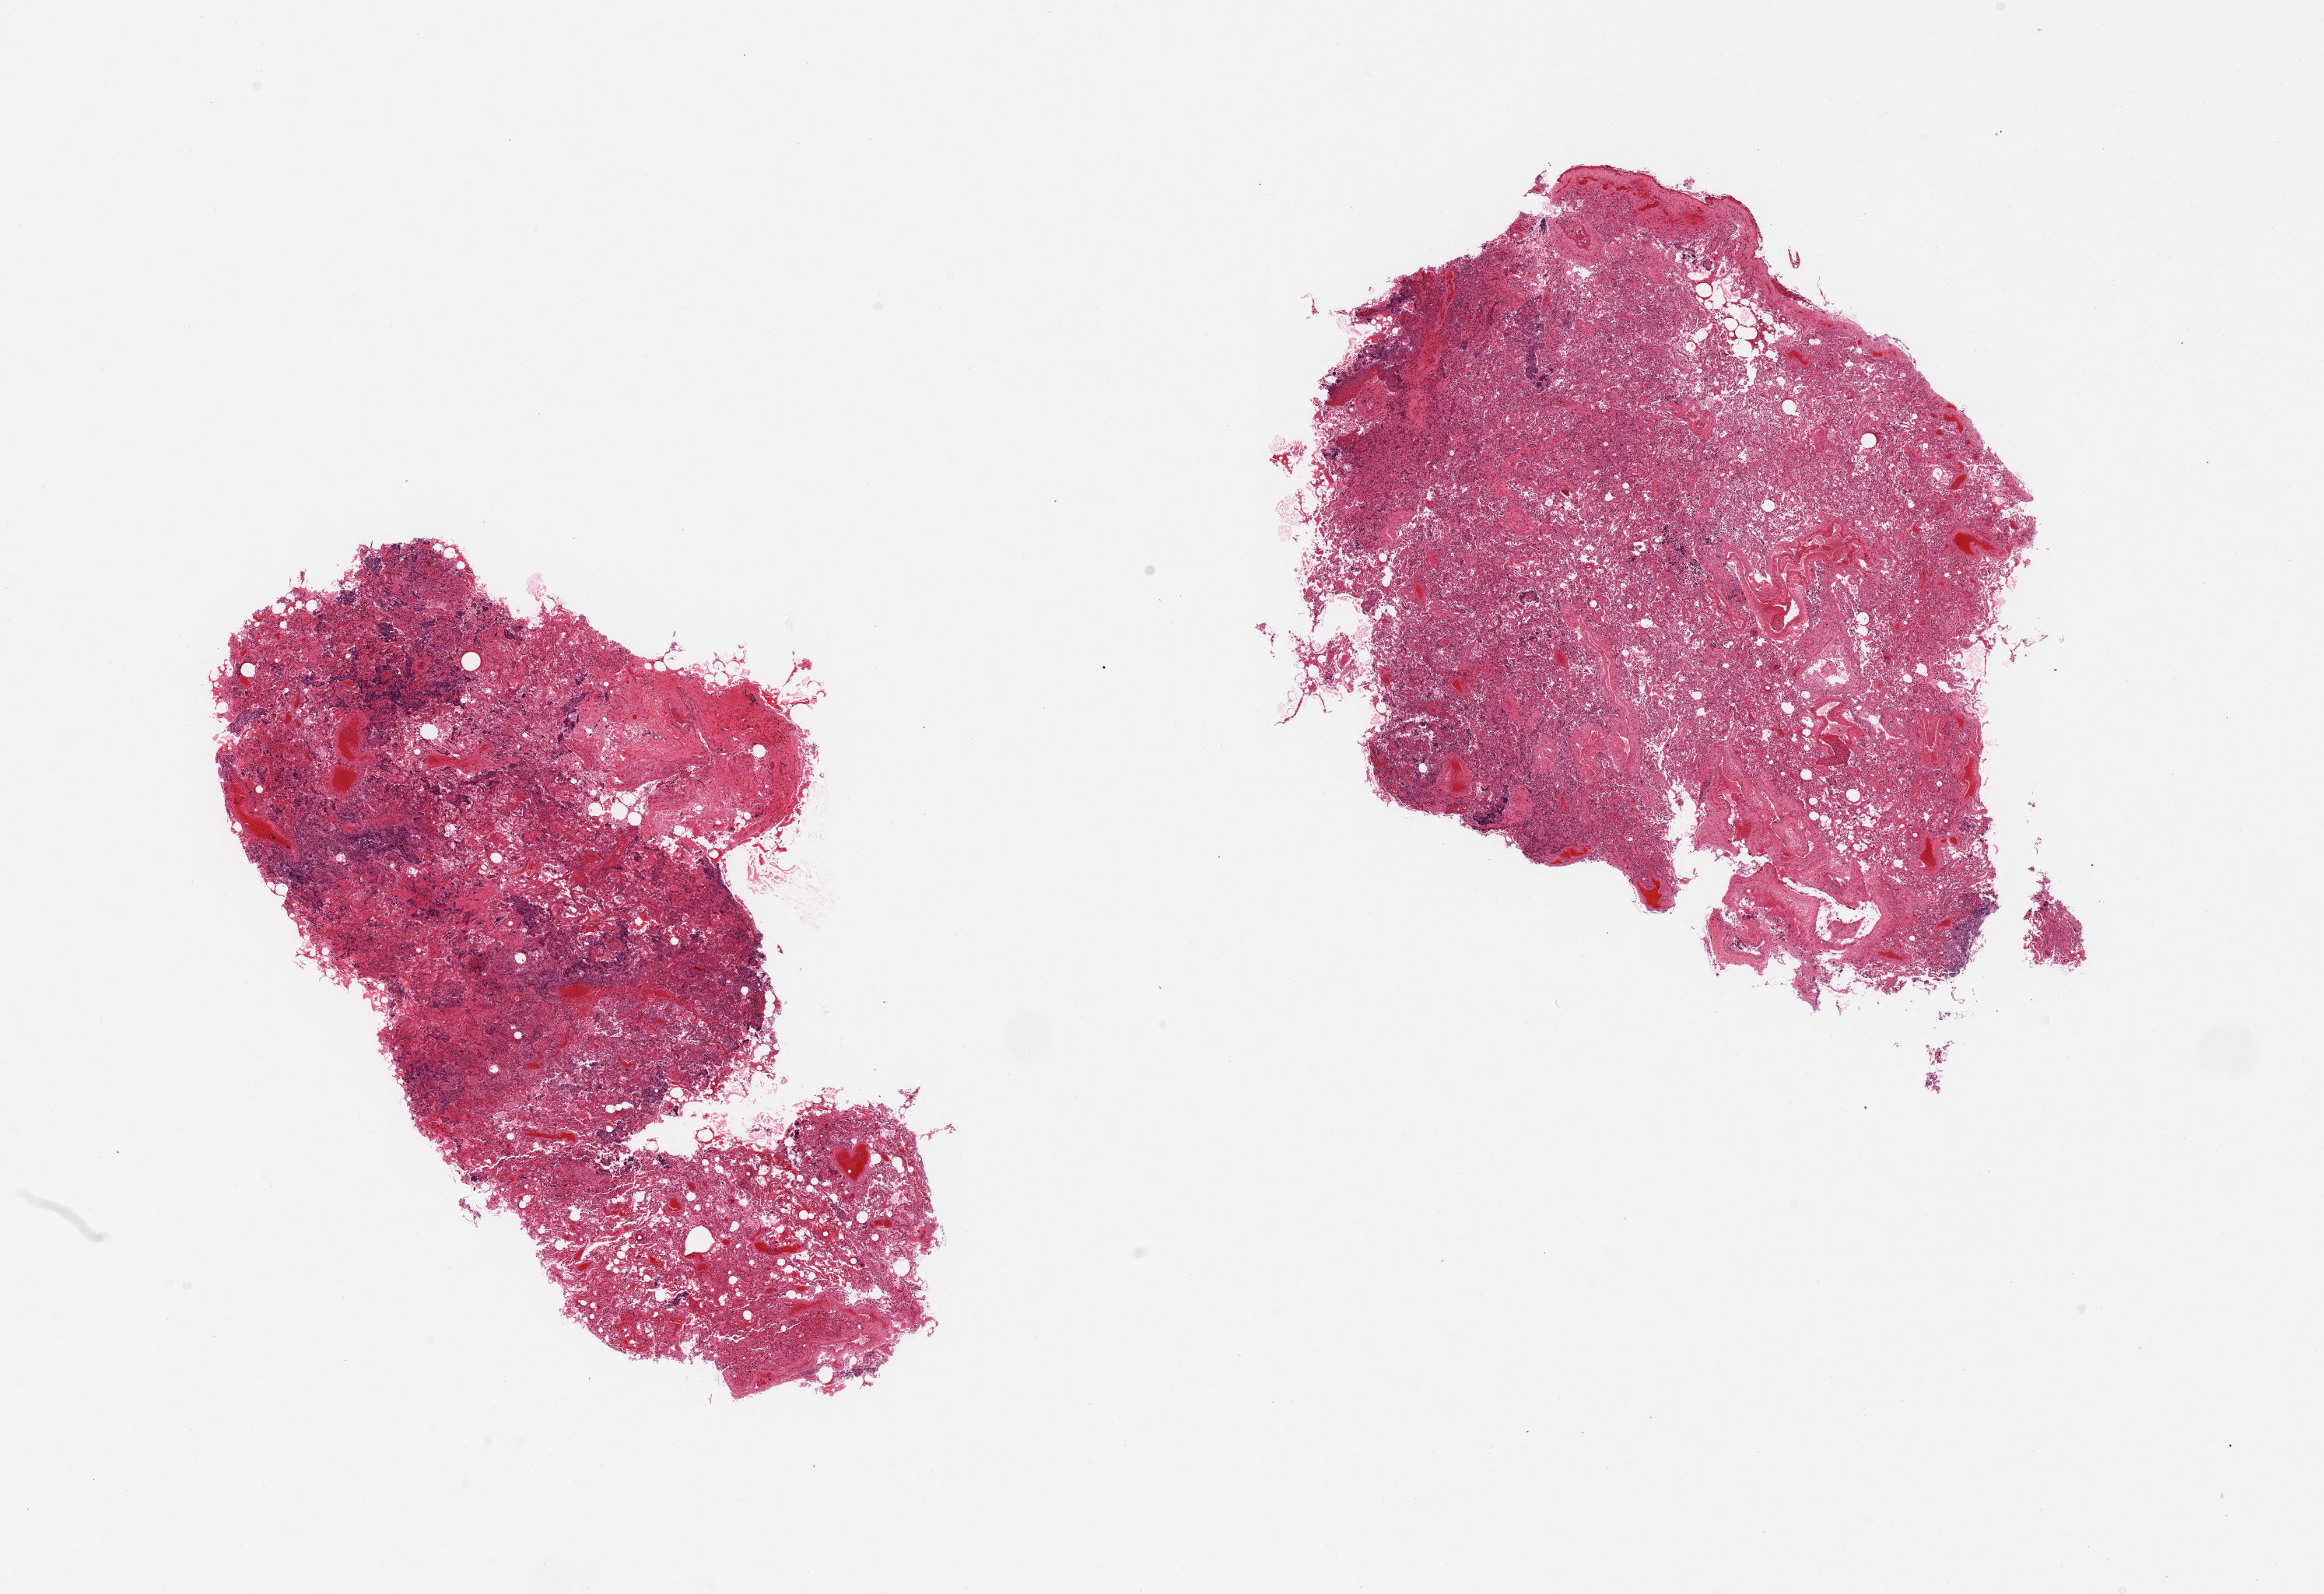
Digitized hematoxylin and eosin (H&E)-stained section — low-resolution overview of the scanned area, about 23.6 x 16.2 mm; PAXgene-fixed paraffin-embedded (PFPE) section; section of lung (target tissue); donor tissue sample. Donor: female.
Pathologist's review note for this sample: 2 pieces diffuse marked acute focally necrotizing pneumonia, marked consolidation/congestion.